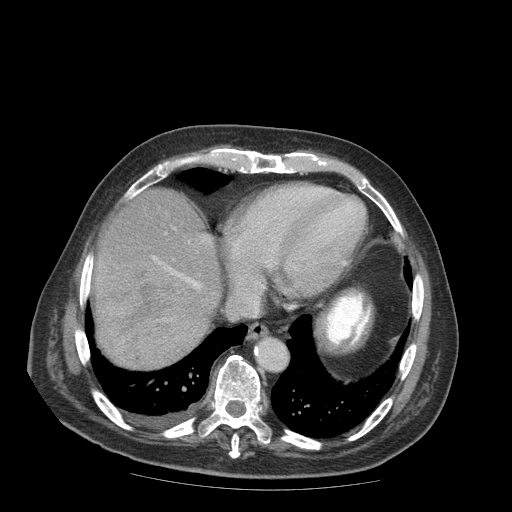
Contrast-enhanced abdominal CT (liver protocol), one axial slice. Position 79 of 99 along the scan axis. Reconstruction kernel STANDARD. Soft-tissue window (W 400 / L 40 HU). 512 × 512 image matrix. Case-level facts recorded for this patient, not image findings: diagnosis: hepatocellular carcinoma (patient treated with transarterial chemoembolisation; whether this scan precedes or follows treatment is not stated here); TNM stage (as recorded): Stage-IIIB; Child-Pugh class: A; tumour nodularity: multinodular.
Structures marked on this image (semi-automatically segmented with operator editing):
- liver parenchyma outside the tumour (the mass and vessels are separate outlines, so this box may not span the whole liver): bounding box (x1, y1, x2, y2) in pixels: (92, 189, 220, 320)
- mass: (95, 250, 215, 371)
- liver vessels: (152, 256, 201, 289)